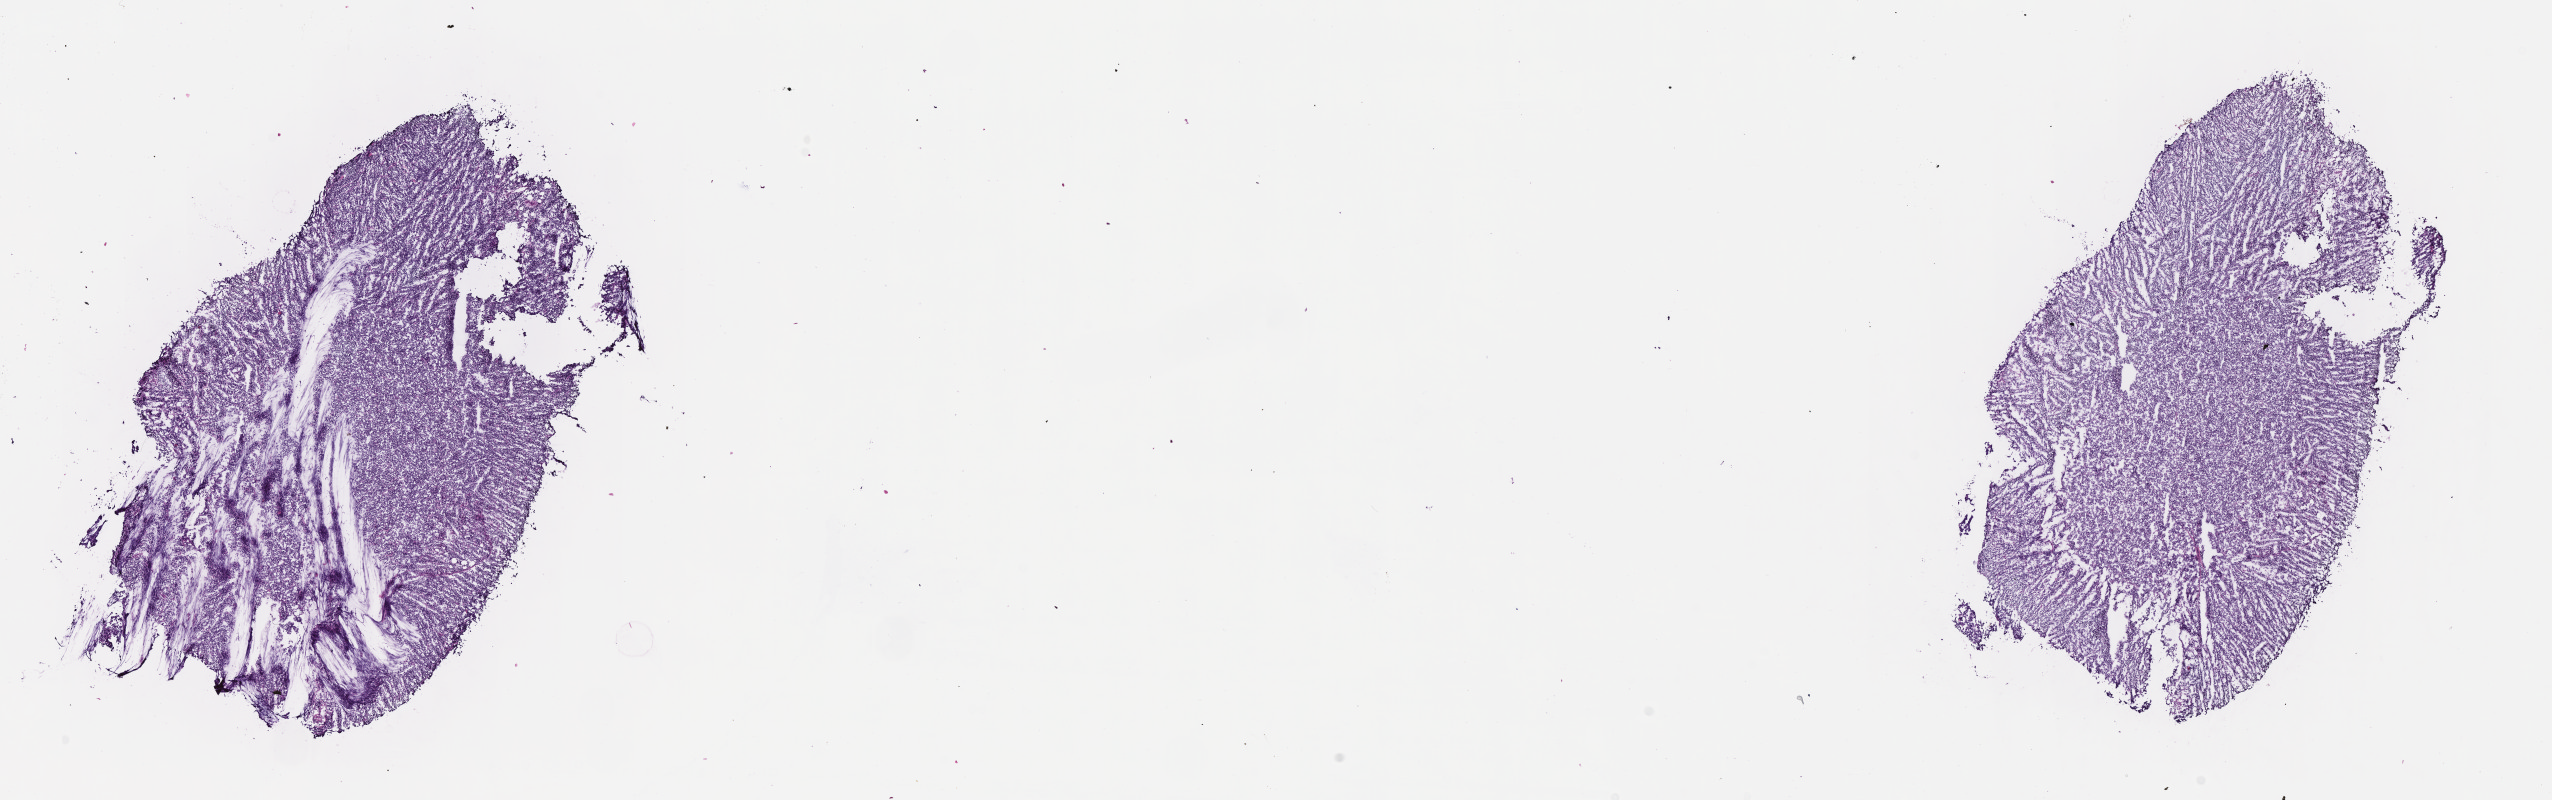
Haematoxylin and eosin whole-slide image, low-resolution overview of the scanned area, about 20.6 x 6.5 mm. Frozen section. Primary tumor. Site: abdominal lymph node. Patient: female, 14 years old. Composition of this section per pathologist review: tumor cells 90%, tumor nuclei 95%, stromal cells 5%, necrosis 5%, normal cells 0%. Infiltration values recorded for this section: lymphocyte infiltration 3%, monocyte infiltration 3%, neutrophil infiltration 0%.
* histologic diagnosis: Burkitt lymphoma, NOS
* Ann Arbor stage (patient): Stage III